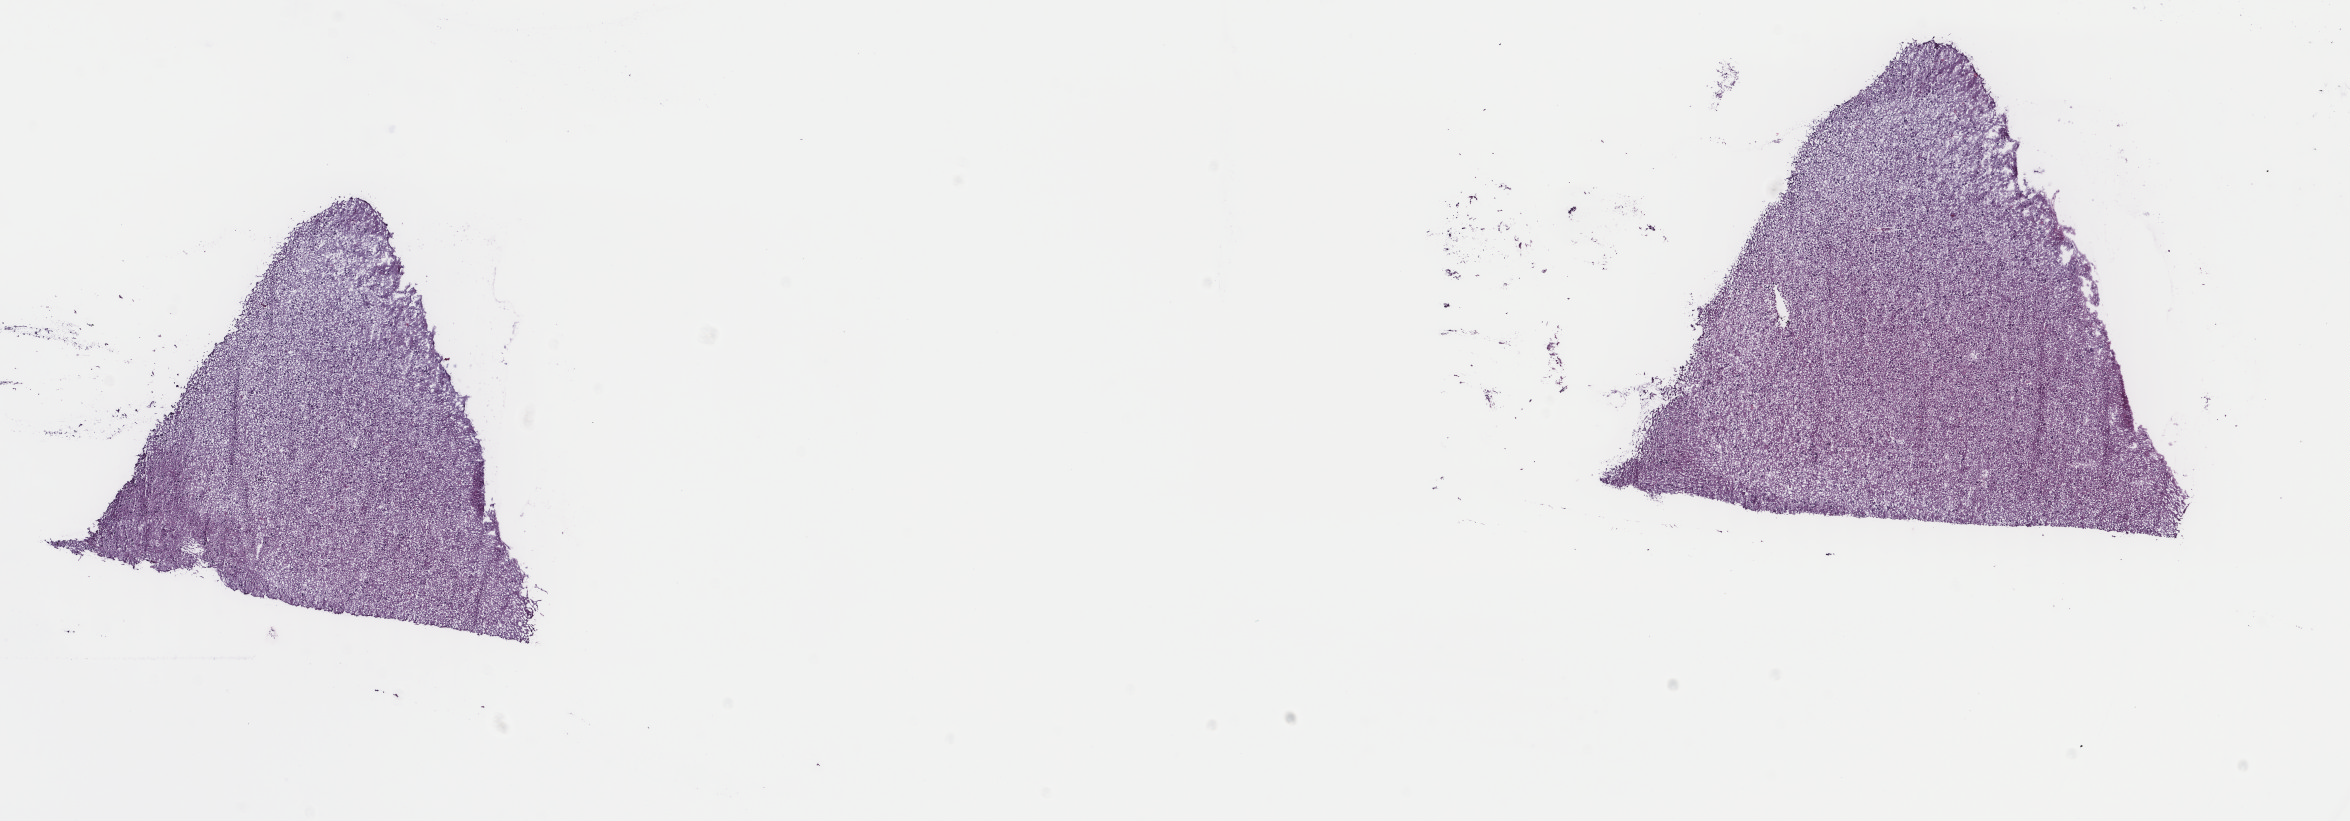
Whole-slide histology image, H&E — whole scanned area (about 18.7 x 6.5 mm) shown as a low-resolution overview; frozen section; sample: primary tumour, brain. Female, age 53 years at initial diagnosis. Histologic grade: G2 (moderately differentiated). Pathologist review of this section (percent, as recorded): tumour cells 60%, tumour nuclei 85%, normal cells 35%, stromal cells 5%, necrosis 0%. Infiltration values recorded for this section: lymphocyte infiltration 0%, monocyte infiltration 0%, neutrophil infiltration 0%.
Pathologic diagnosis: Mixed glioma. Laterality: left.